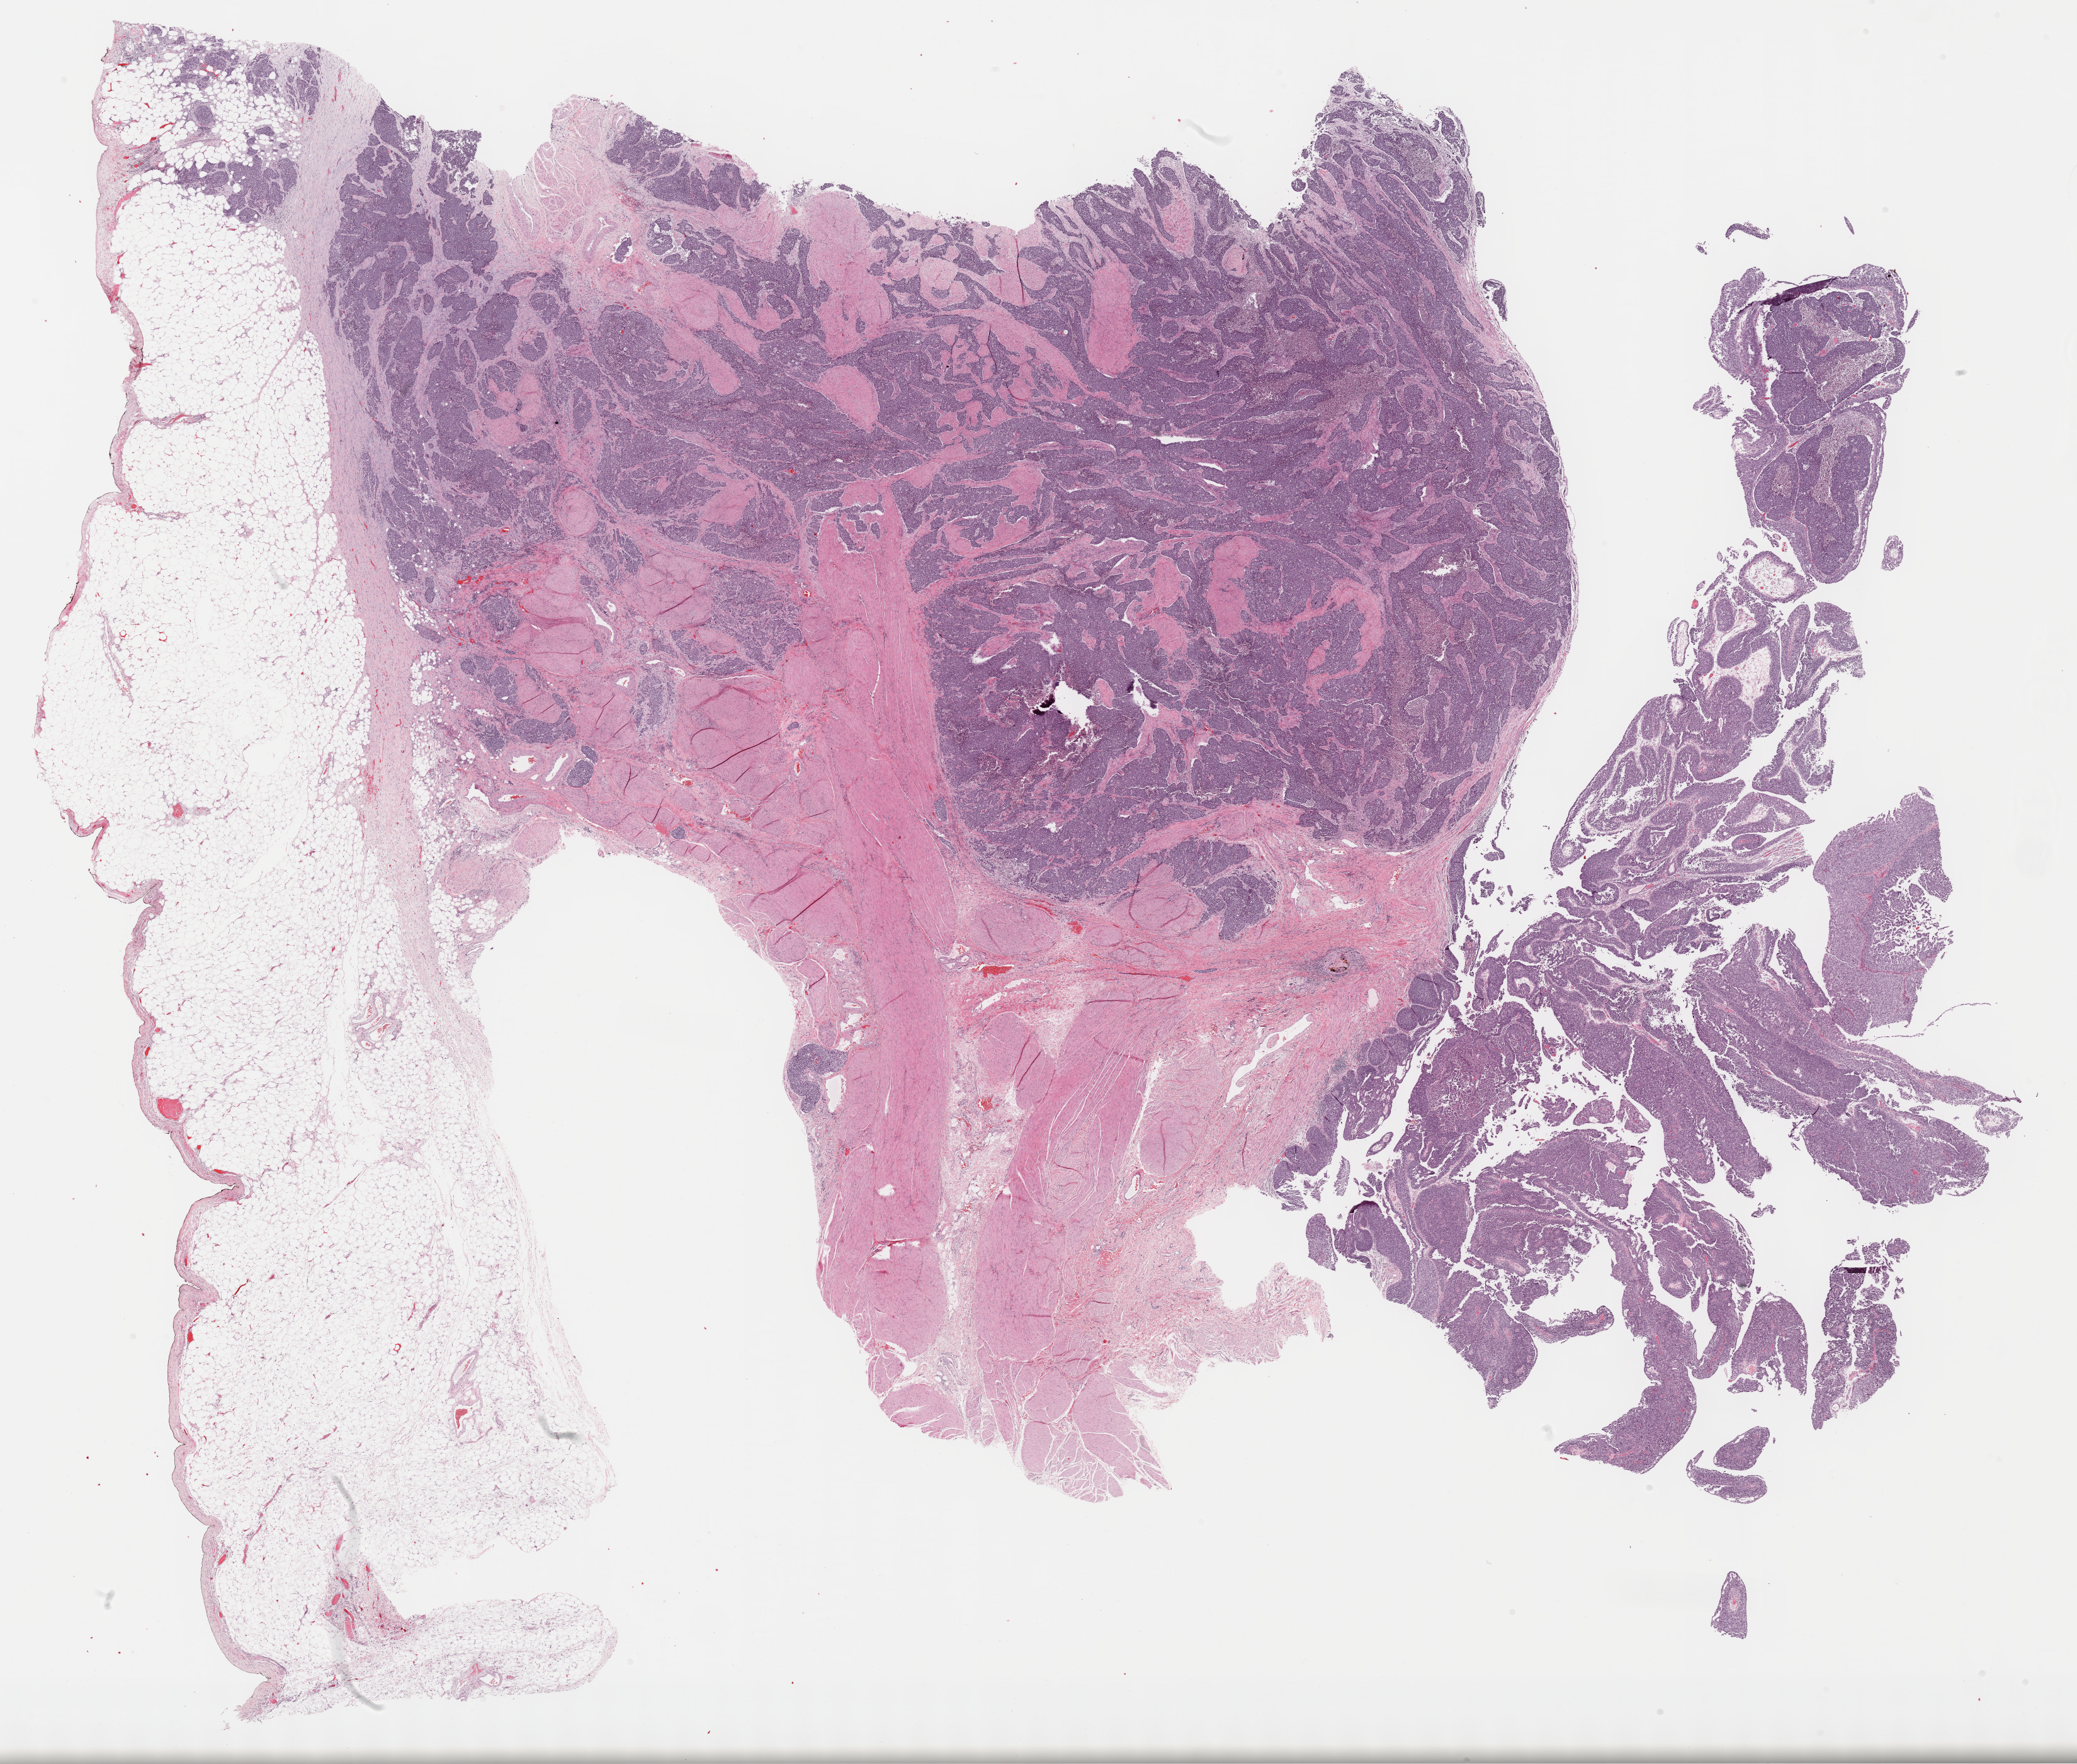
Whole-slide histology image, Hematoxylin and eosin (H&E) stained — low-resolution overview of the scanned area, about 26.7 x 22.7 mm (from a 40x scan). Formalin-fixed paraffin-embedded (FFPE) diagnostic section. Bladder, primary tumour sample. Male, age 85 years at initial diagnosis. Histologic grade: high grade.
- lymph nodes positive (case pathology): 2 of 18 examined
- histologic diagnosis: Transitional cell carcinoma
- AJCC pathologic stage: IV (6th edition)